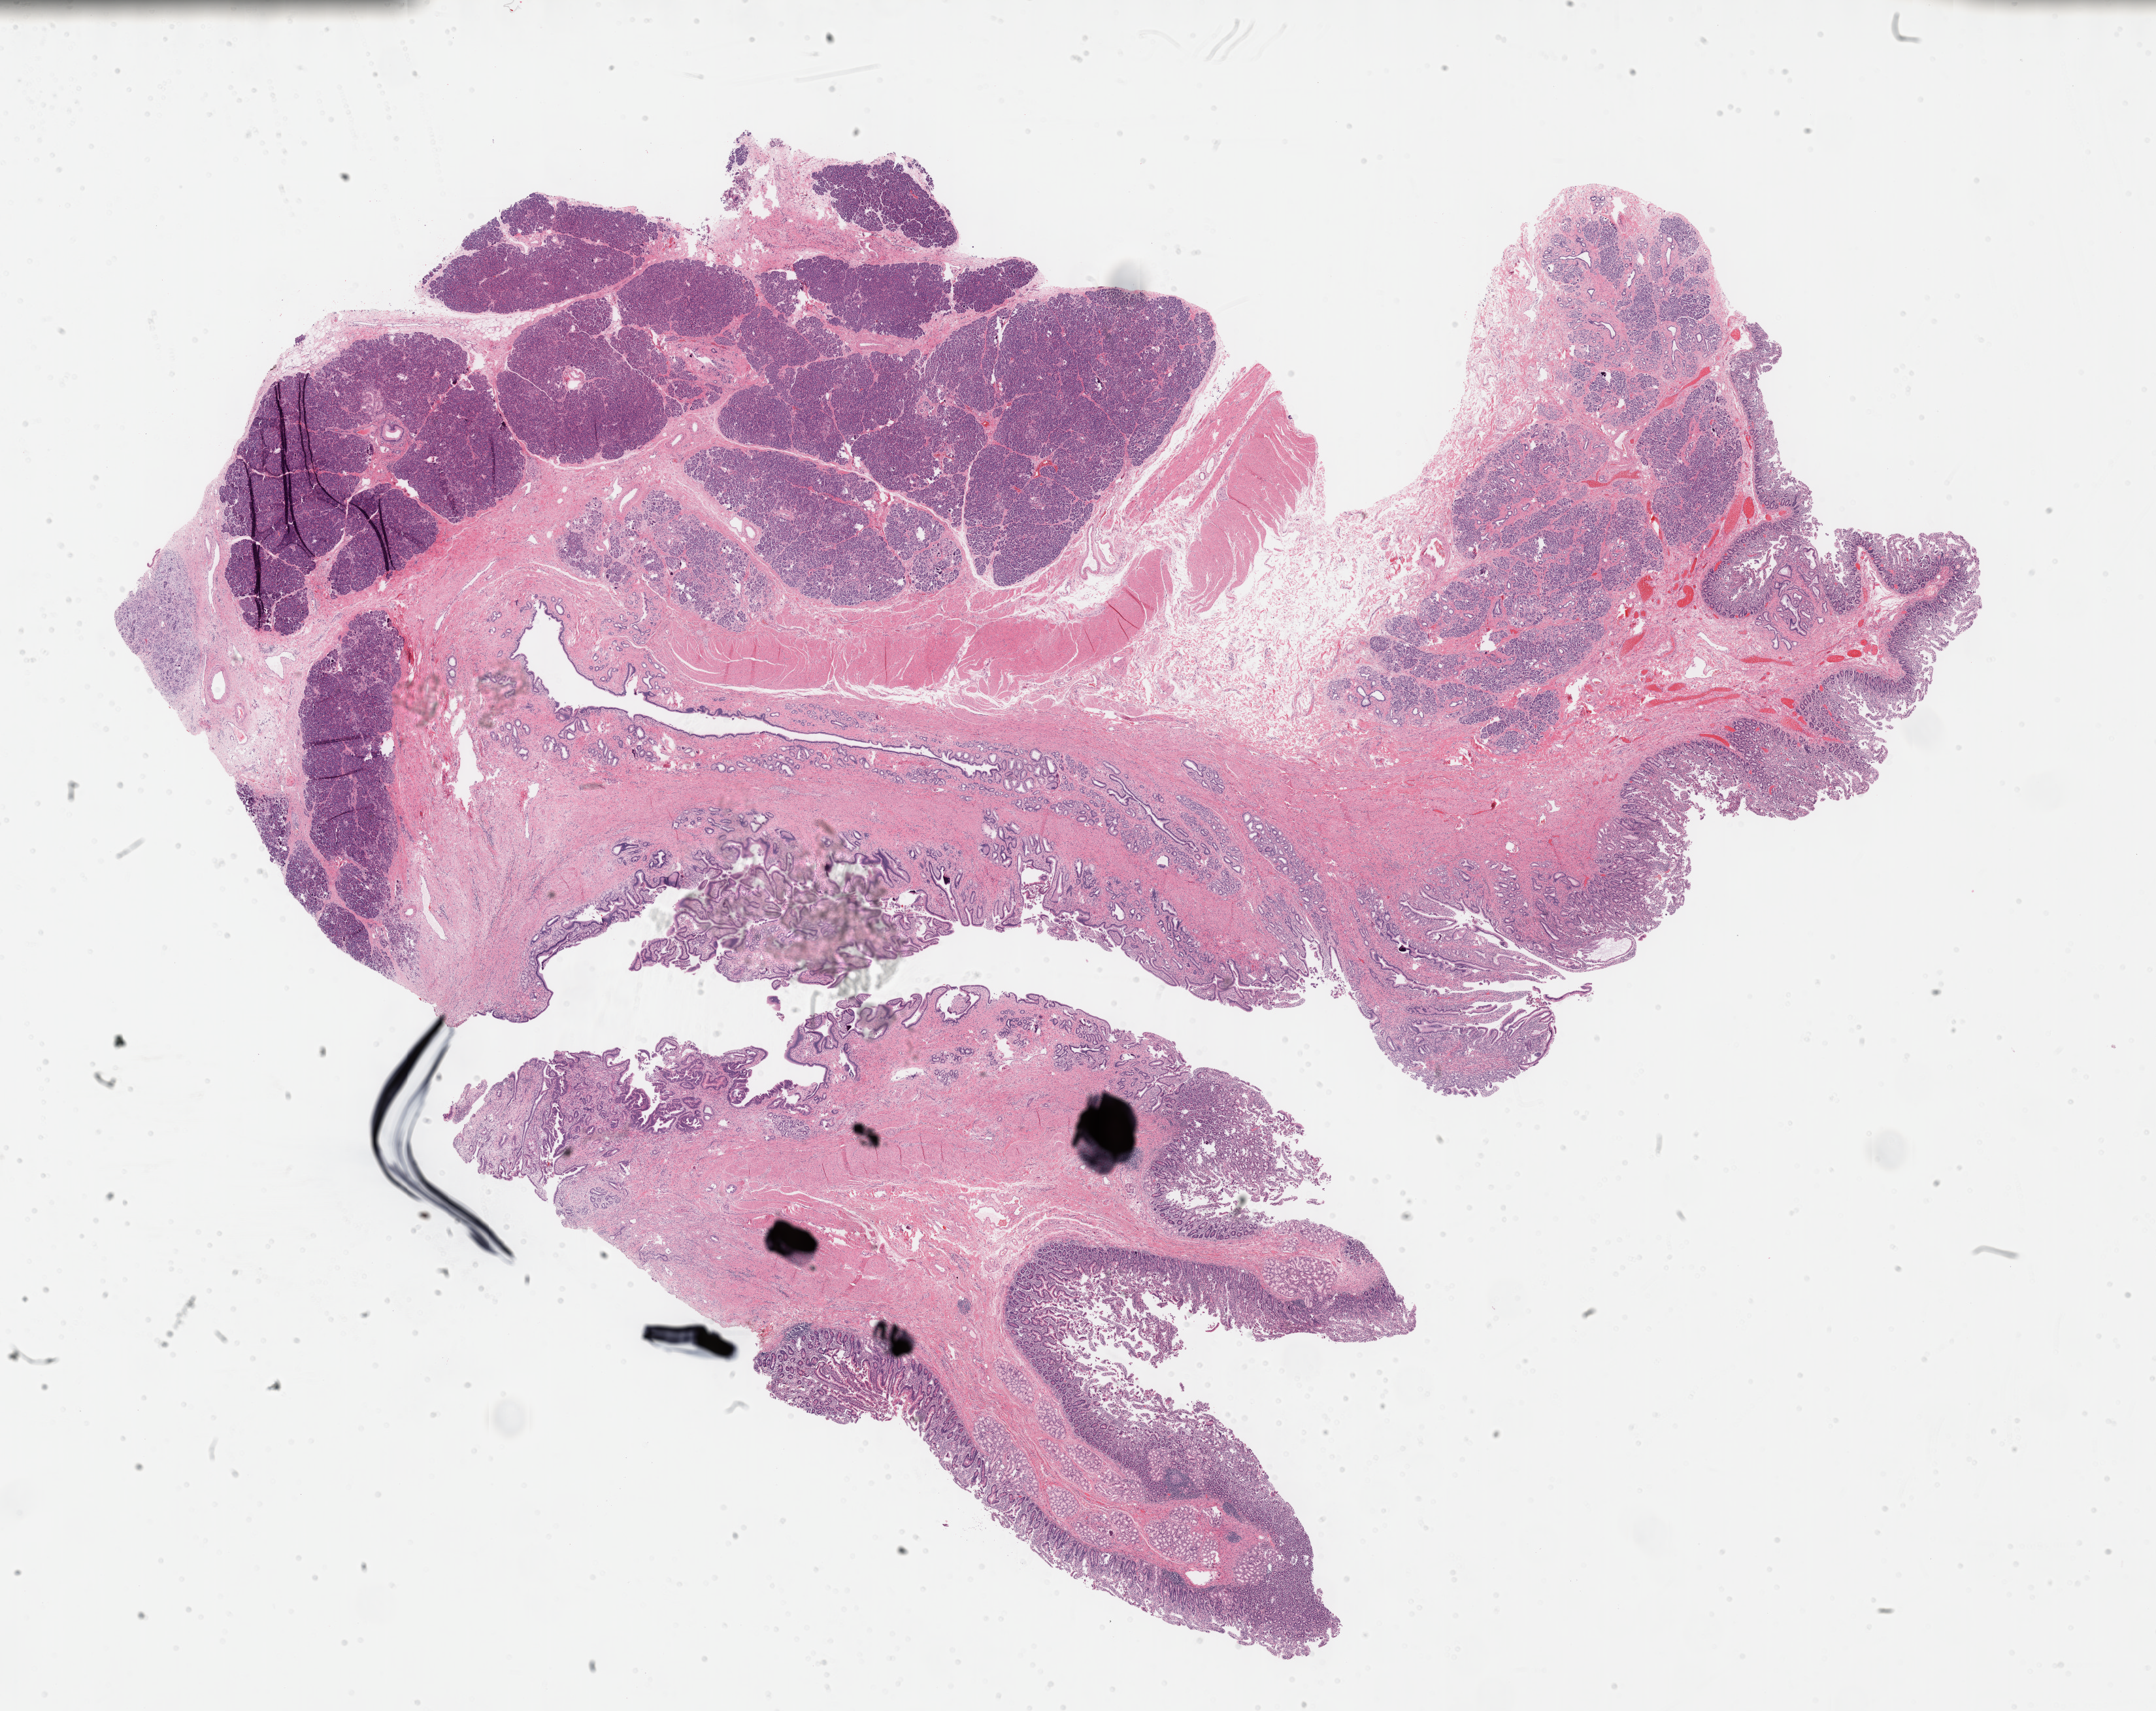
Whole-slide histology image, H&E-stained, a low-resolution overview of the entire scanned area, about 26.7 x 21.2 mm (from a 40x scan). Formalin-fixed paraffin-embedded (FFPE) diagnostic section. Primary tumour sample from the pancreas. Patient: female, age at initial diagnosis 57 years. Histologic grade: G2 (moderately differentiated).
• diagnosis: Infiltrating duct carcinoma, NOS (head of pancreas)
• AJCC pathologic stage: IIB
• TNM: T3 N1 M0
• lymph nodes positive (case pathology): 7 of 30 examined